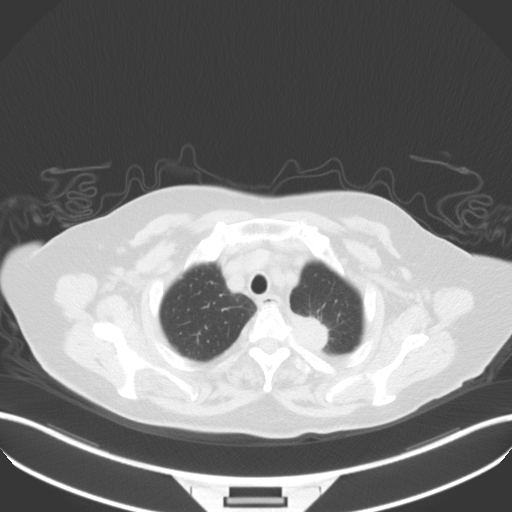
Chest CT, one axial slice. Slice 42 of 50 in the series (ordered by position). Reconstruction kernel B31f. Lung window (W 1500 / L -600 HU). 512 × 512 image matrix. Patient: female, 81 years. From the clinical record (not read from this slice): clinical TNM (as recorded): T2a N0 M0.
Annotated regions visible in this slice (bounding box drawn by a radiologist):
- lung tumour (recorded histology: adenocarcinoma): bounding box <295,312,332,356> (left, top, right, bottom; pixels)